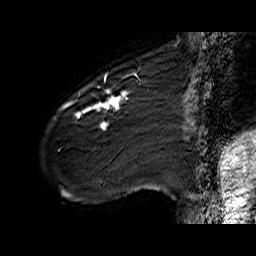
Breast MRI (dynamic contrast-enhanced), one sagittal slice. Slice 14 of 60 in the series (ordered by position). Dynamic contrast-enhanced series, time point 2 of 6 at this slice position (early post-contrast). 1.5 T. TE 6.4 ms, TR 32.9 ms. 256 × 256 image matrix, field of view 200 × 200 mm. Female patient. Case-level facts recorded for this patient, not image findings: setting: breast cancer imaged before/during neoadjuvant chemotherapy; receptor status: HER2-positive.
Outlined on this slice (semi-automatic segmentation, software-assisted and operator-edited):
- analysis volume of interest (the breast-tissue region the enhancement analysis was run in; not a lesion): box from (x=61, y=77) to (x=141, y=142) px
- tumour enhancement mask (voxels above the 100 % enhancement threshold inside the analysis volume of interest): (x=61, y=77)–(x=129, y=129)